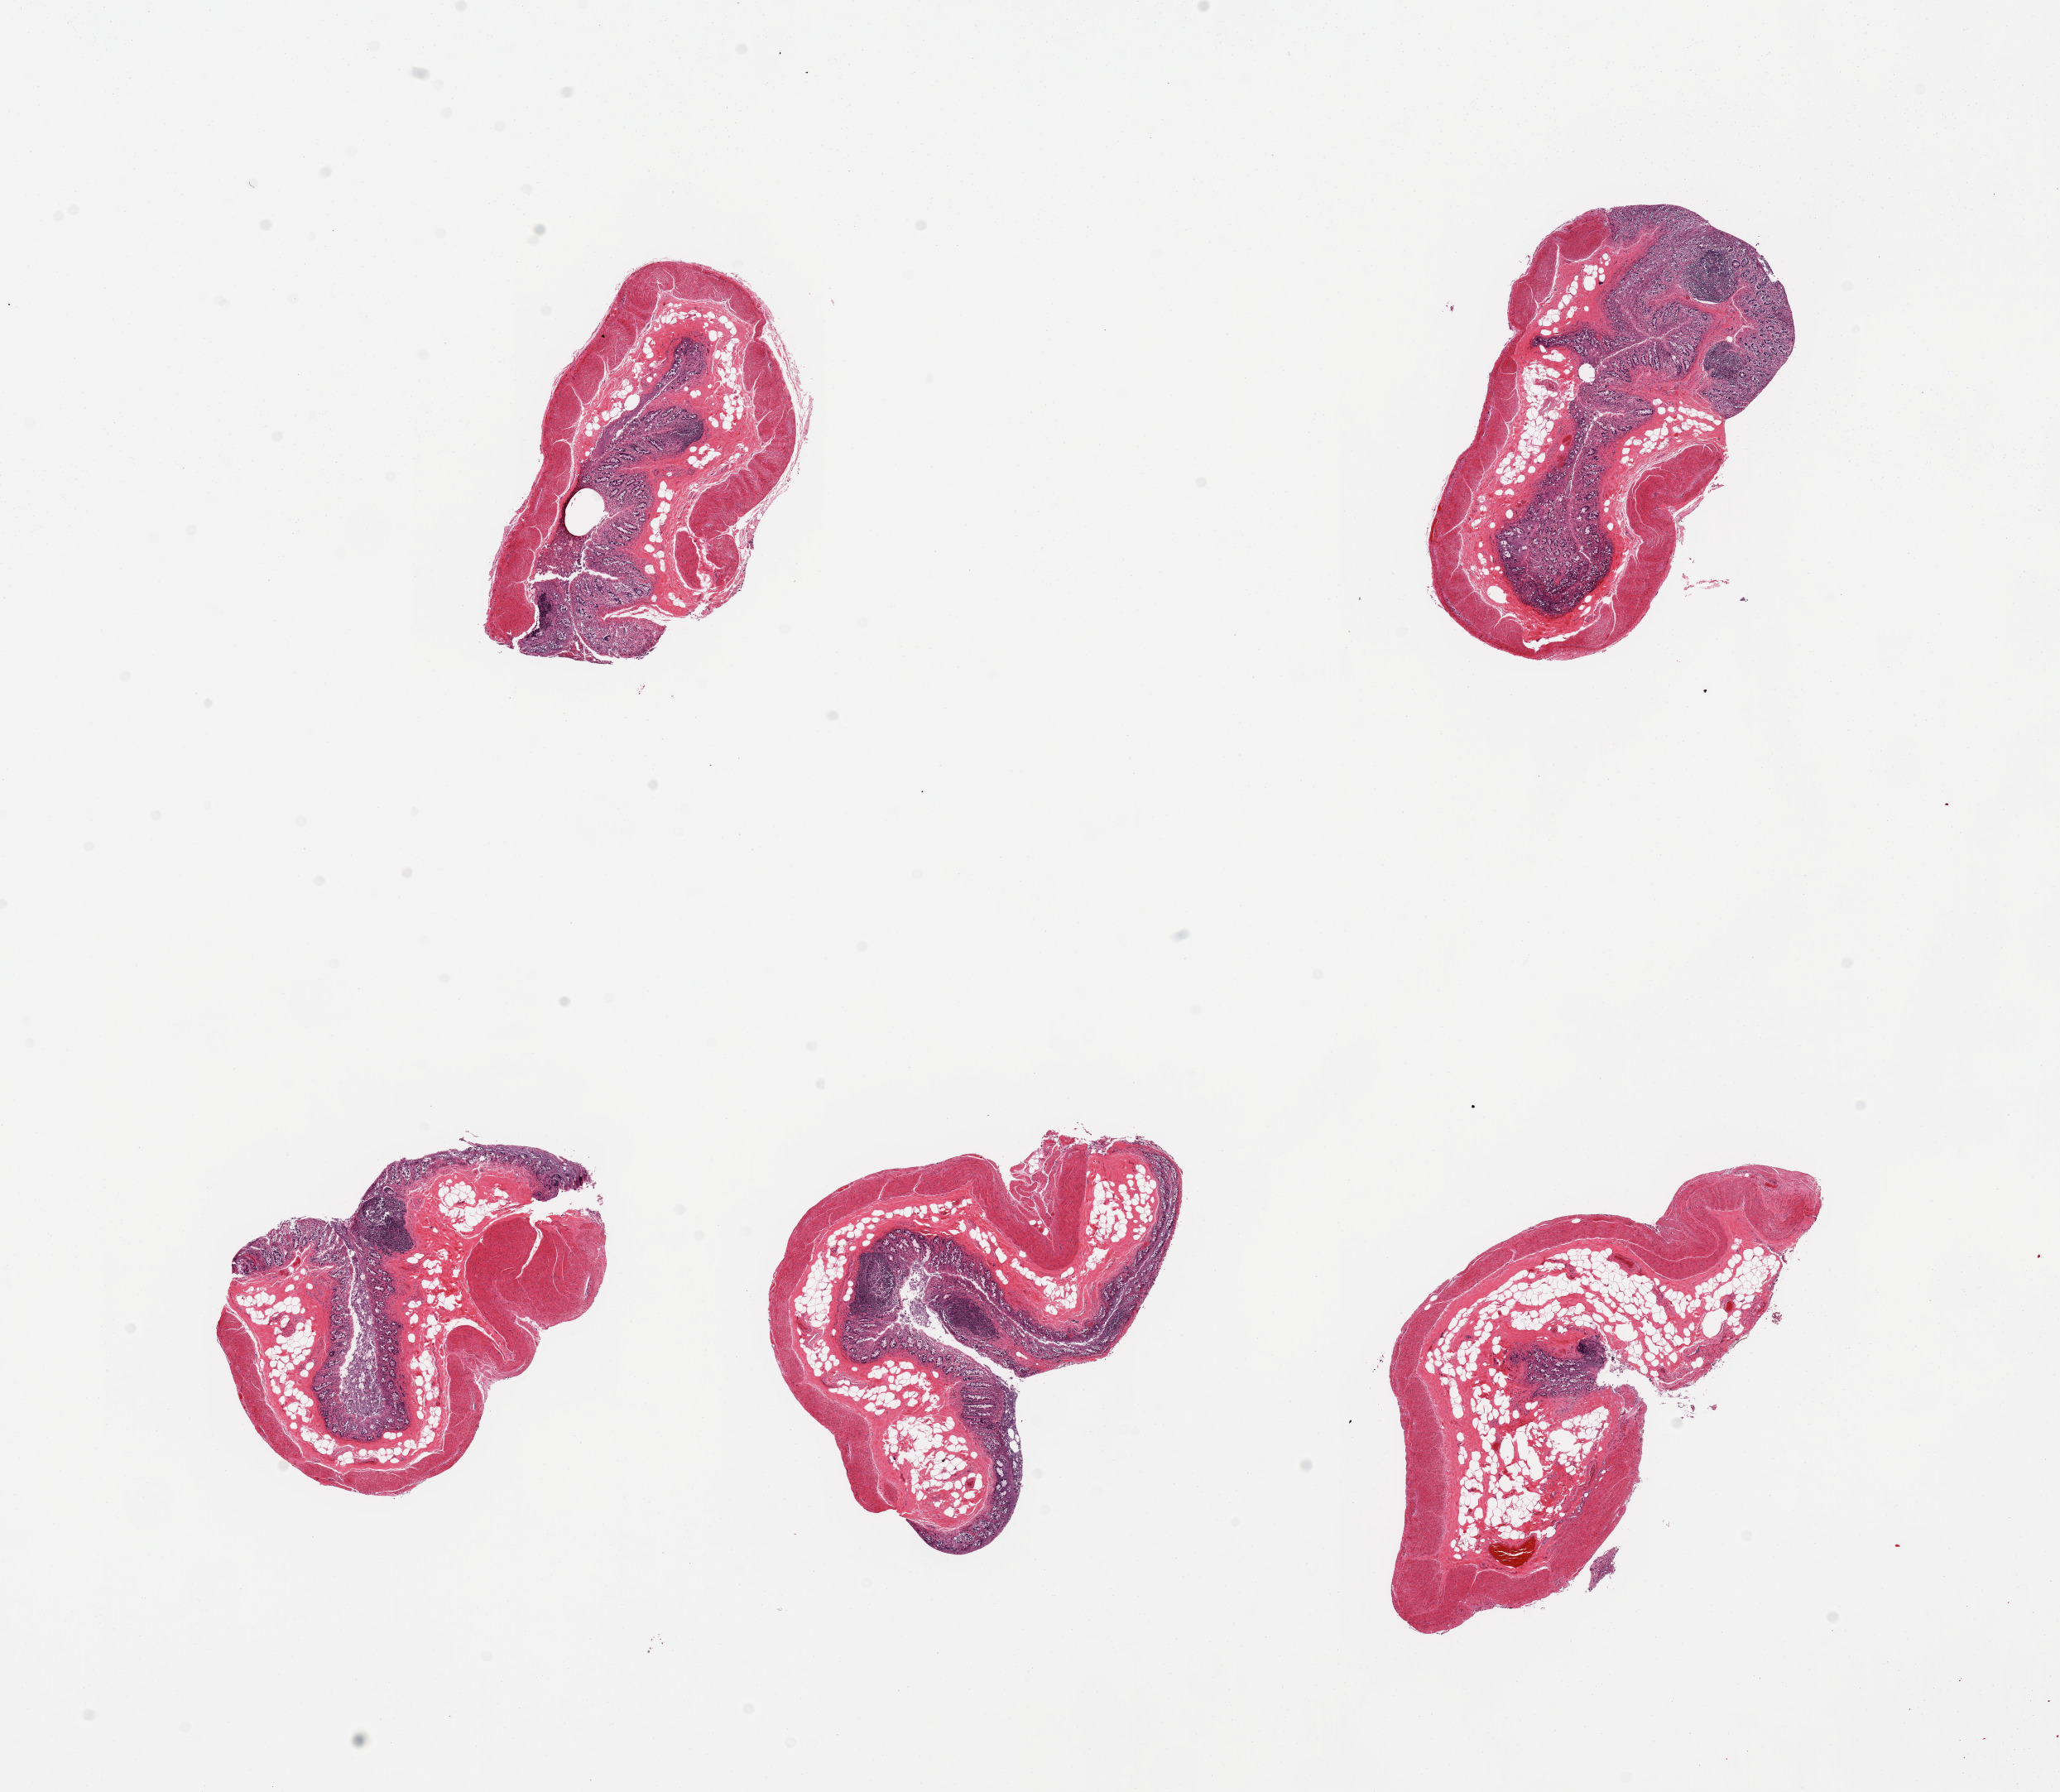
Hematoxylin and eosin (H&E) whole-slide image, low-resolution overview of the scanned area, about 19.7 x 17.1 mm, PAXgene-fixed paraffin-embedded (PFPE) section, section of transverse colon (target tissue), tissue donor sample. Male donor.
Review note (as recorded): 5 pieces; mucosa severely autolyzed, muscularis slightly autolyzed; abundant [20 to 50%] submucosal fat.